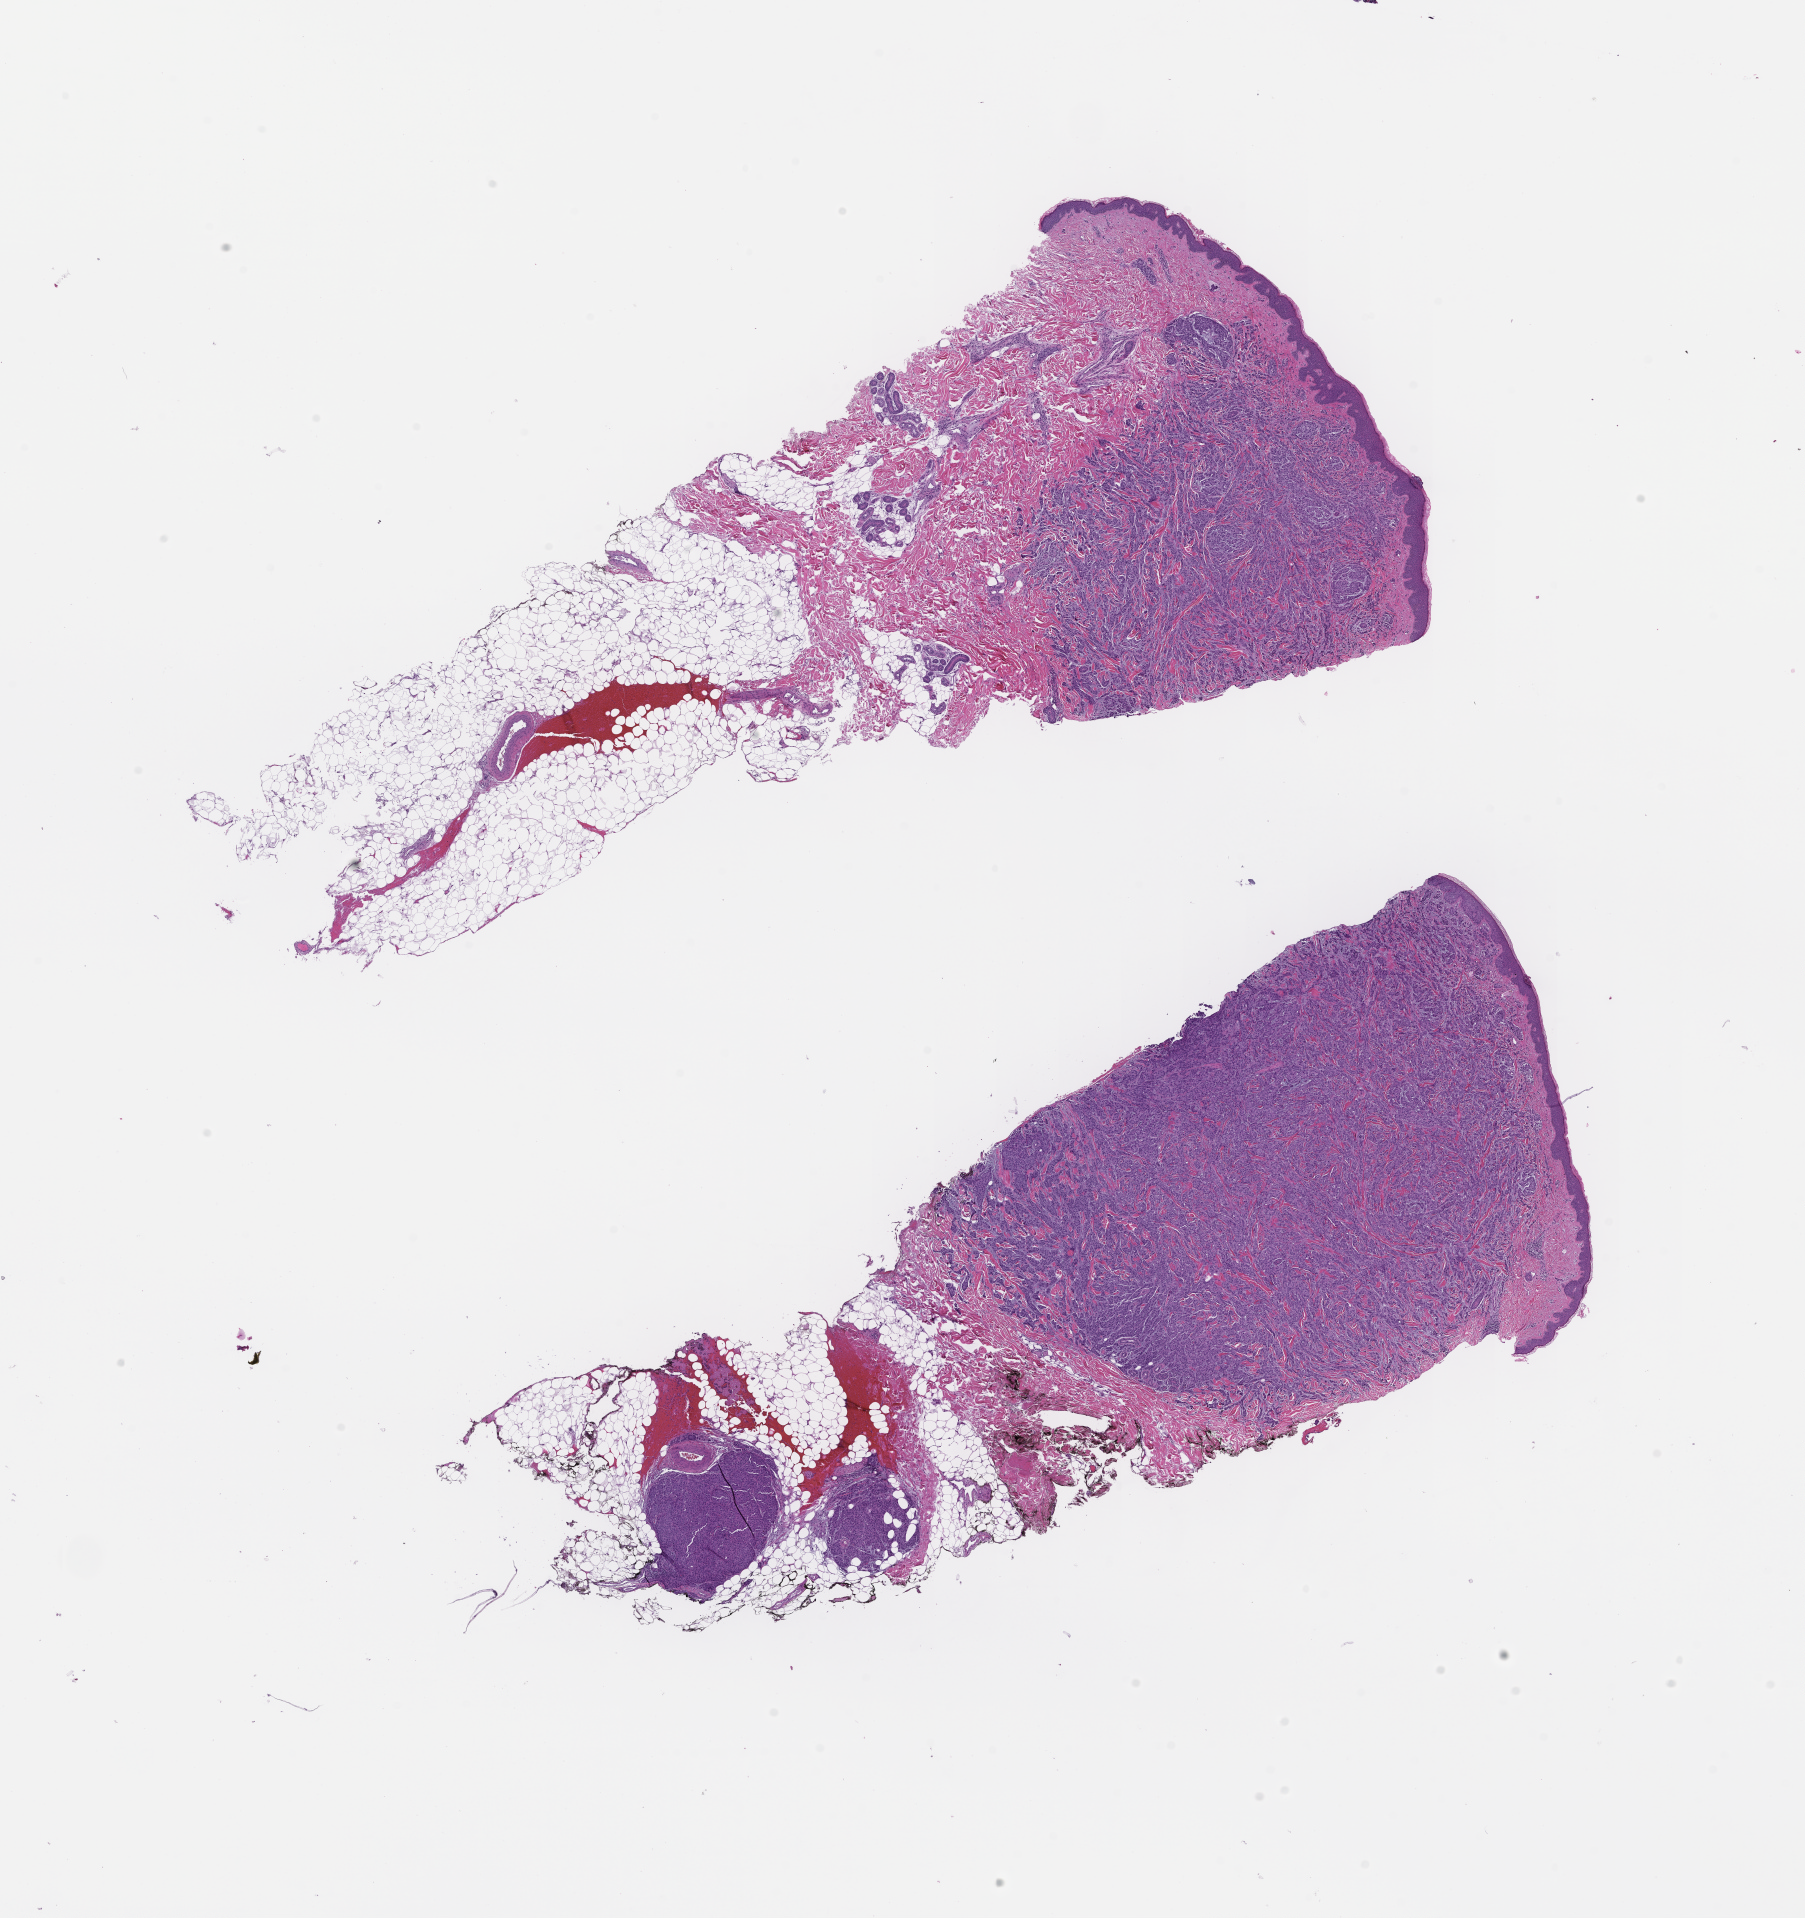
Whole-slide image, H&E stain — whole scanned area (about 14.6 x 15.5 mm) shown as a low-resolution overview. Formalin-fixed, paraffin-embedded (FFPE) tissue. Archival tissue. Female patient.
This section: metastatic tumor tissue. Patient diagnosis (primary): Invasive Breast Carcinoma.